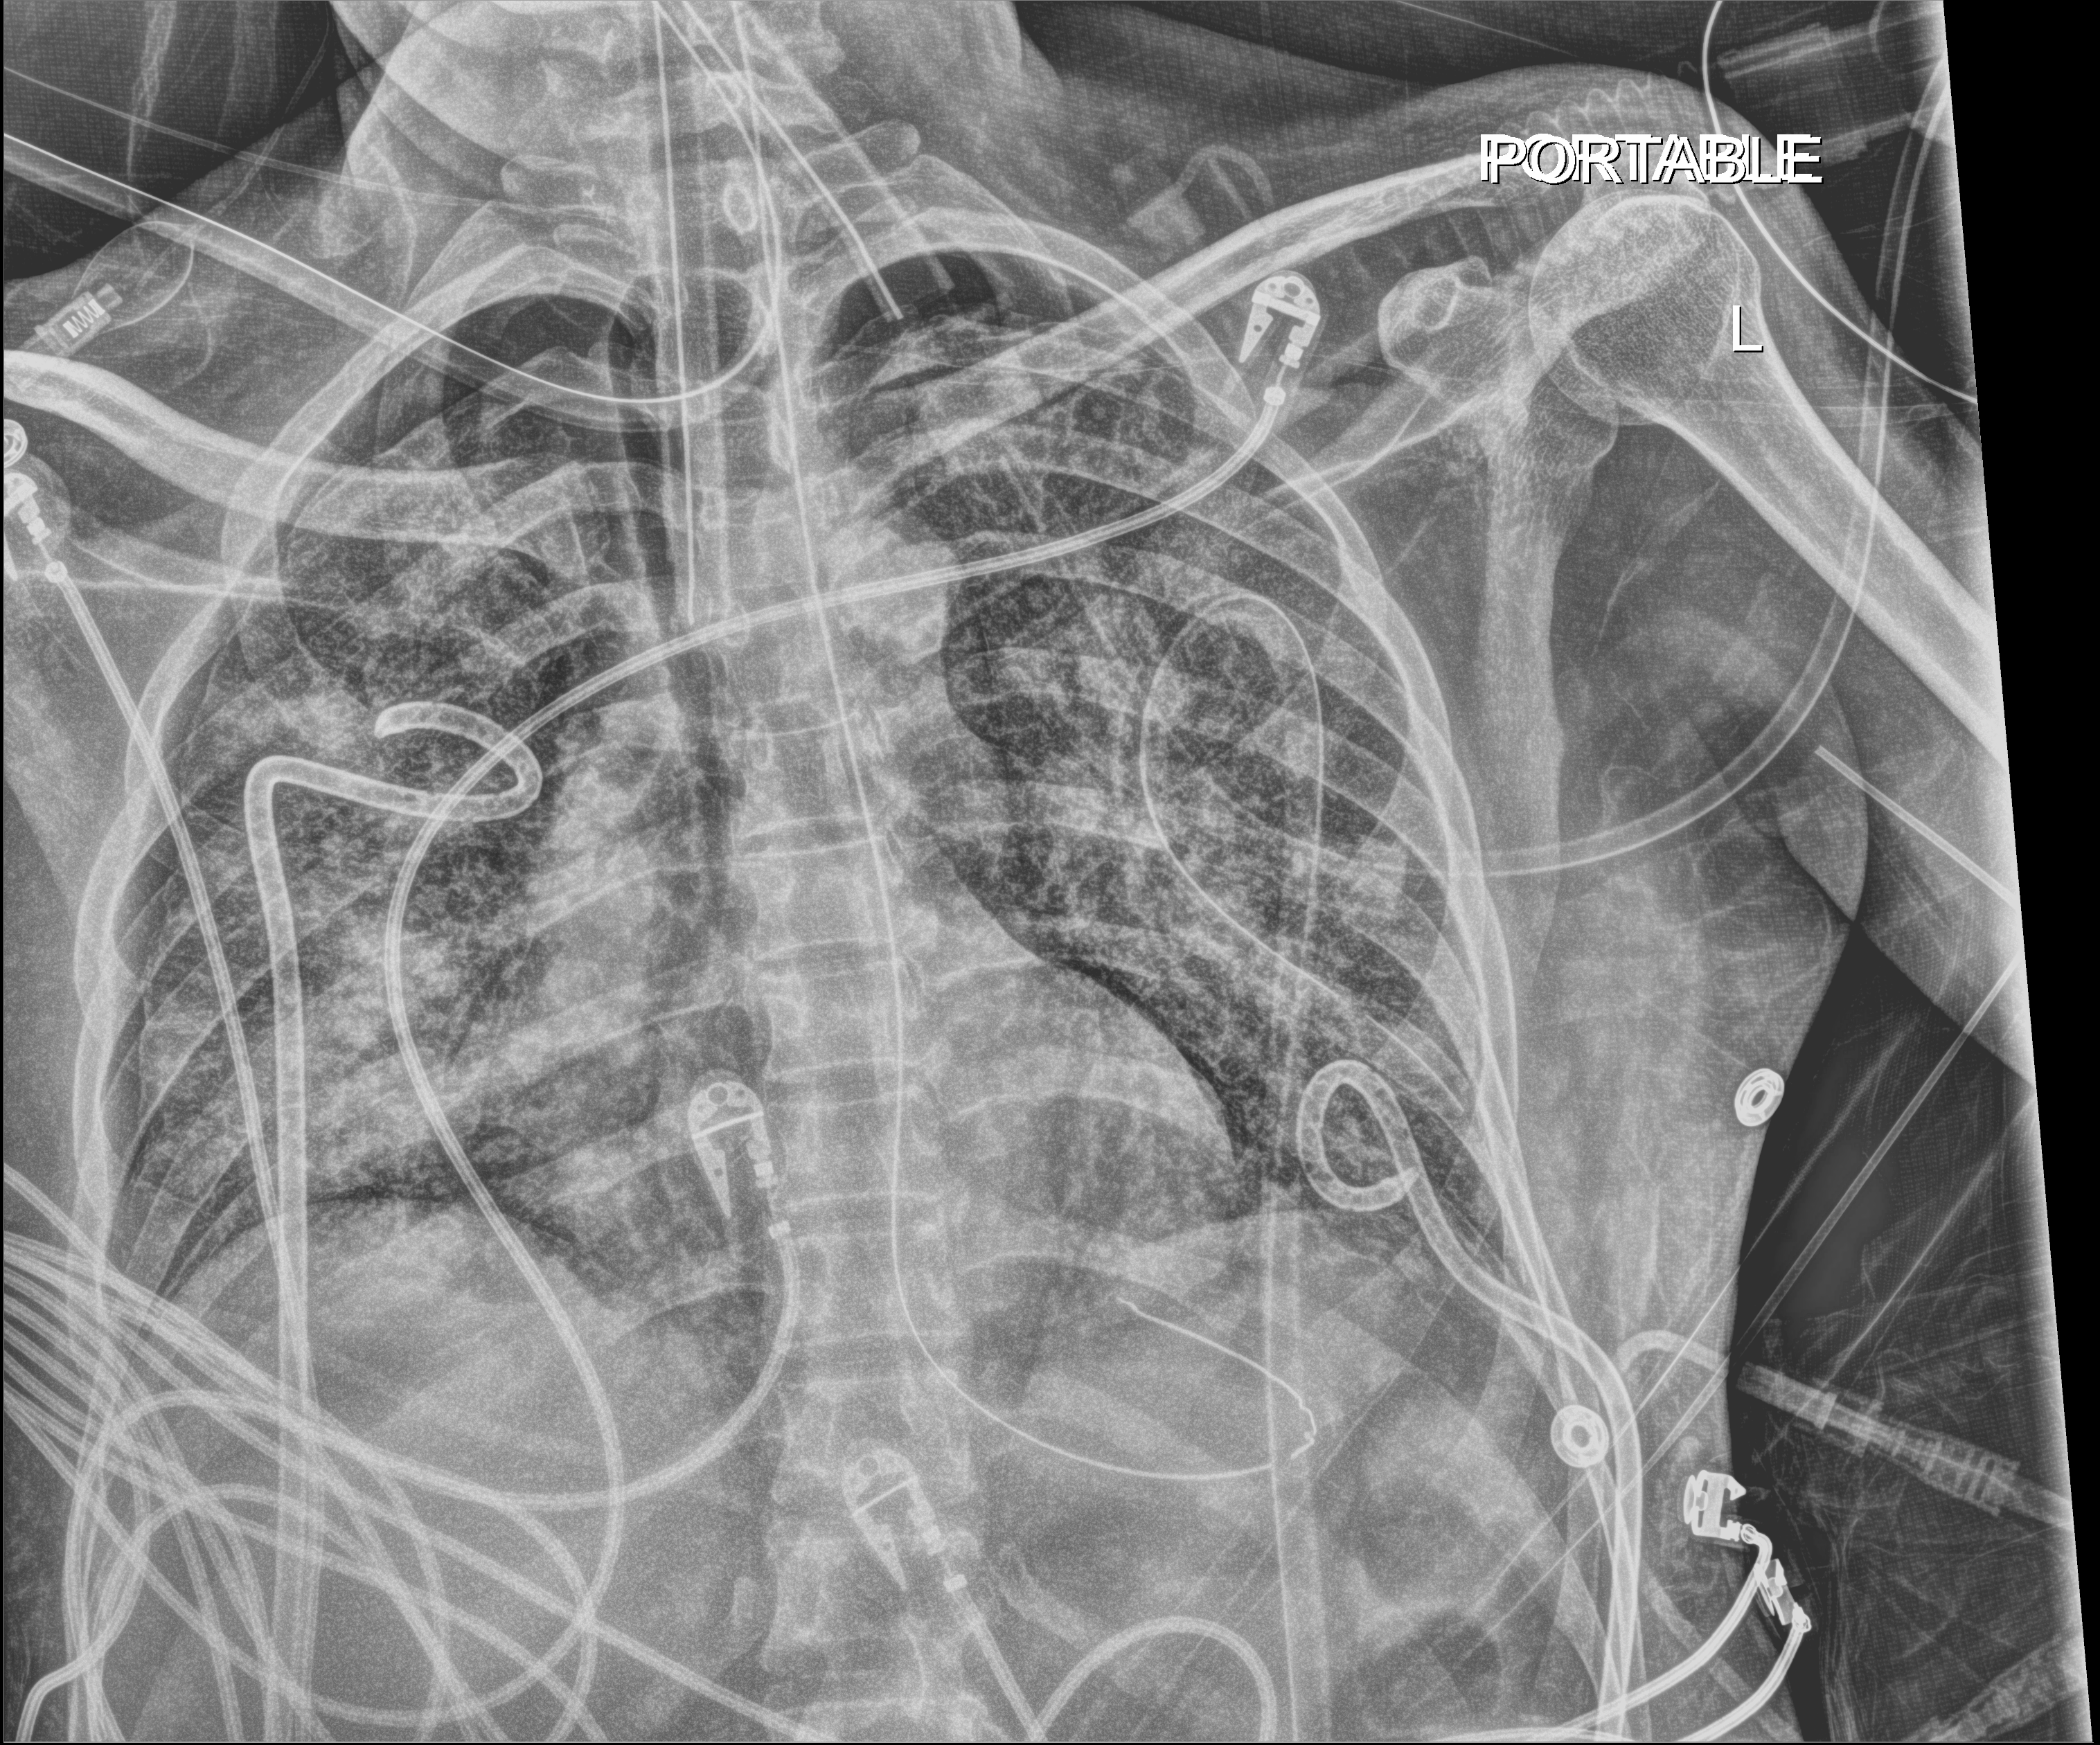
Chest radiograph; anteroposterior (AP) projection. Patient hospitalised with COVID-19, aged 18–59 years.
Admission-level facts for this patient (not findings on this image; timing relative to this image not recorded): COPD (admission record): no; admitted to intensive care during this hospital stay: yes.